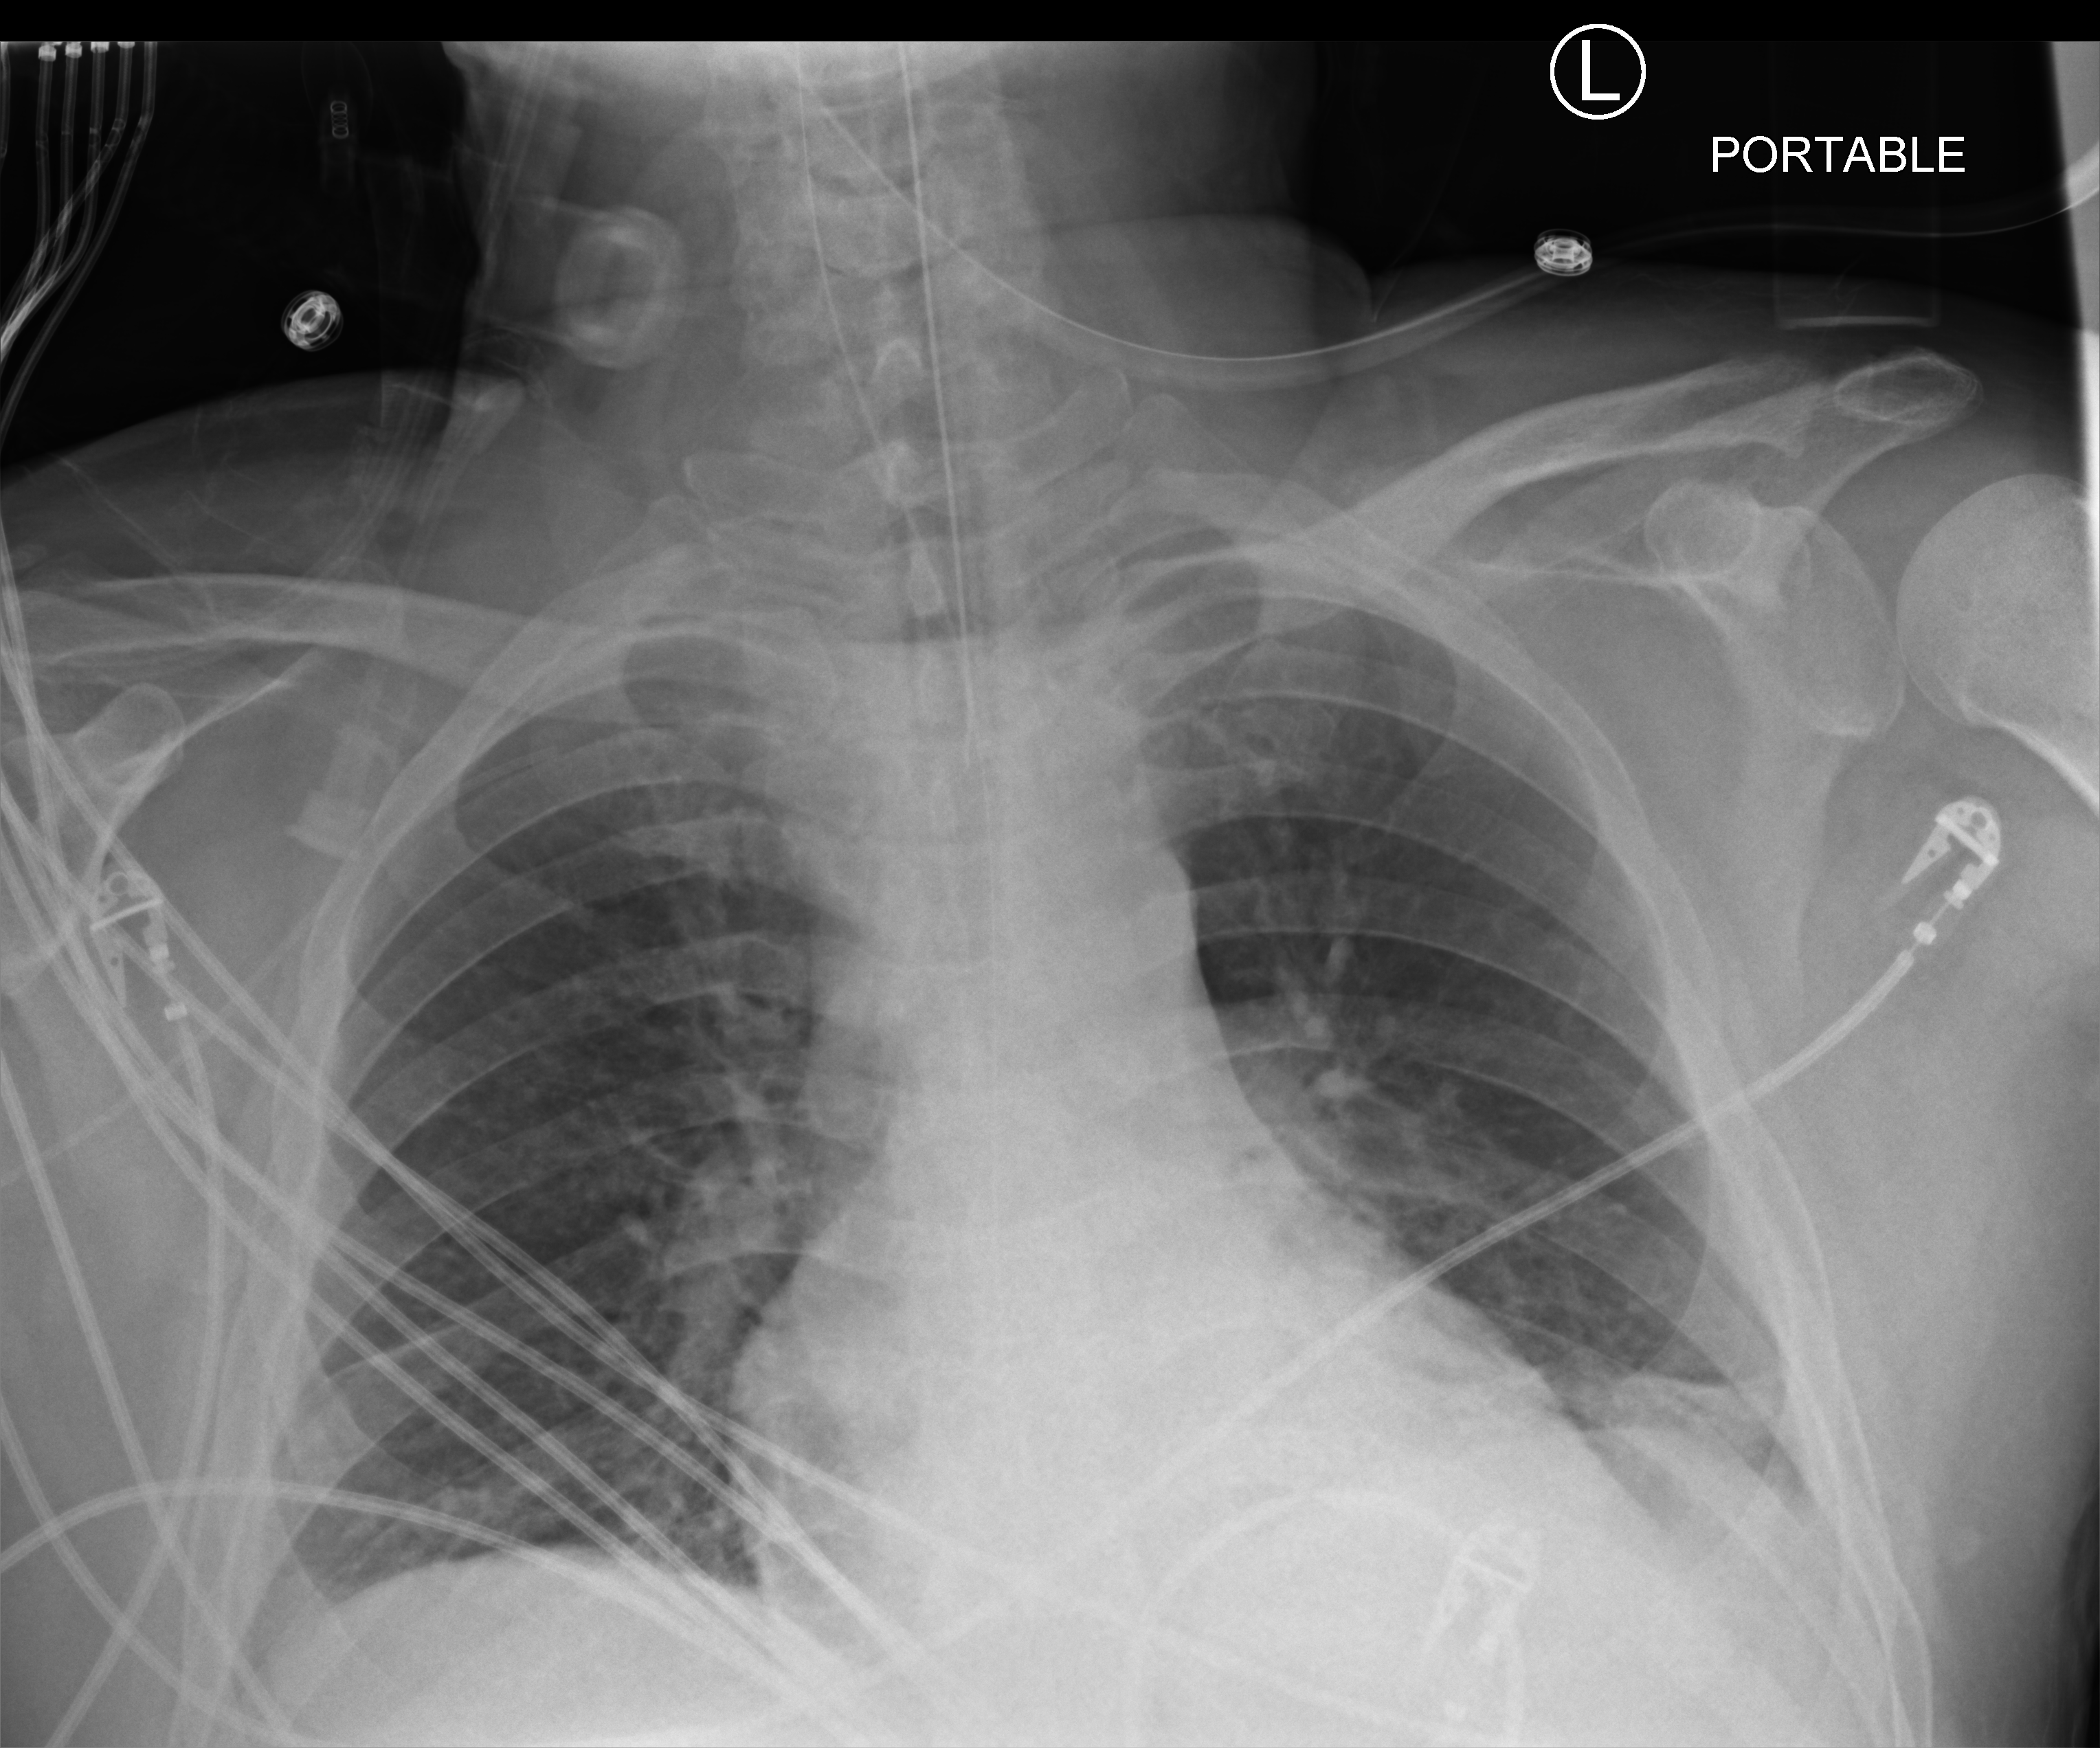
Chest X-ray (portable); anteroposterior (AP) projection. Patient hospitalised with COVID-19; male, aged 18–59 years.
Admission-level facts for this patient (not findings on this image; timing relative to this image not recorded):
- admitted to intensive care during this hospital stay: yes
- mechanically ventilated during this hospital stay: yes